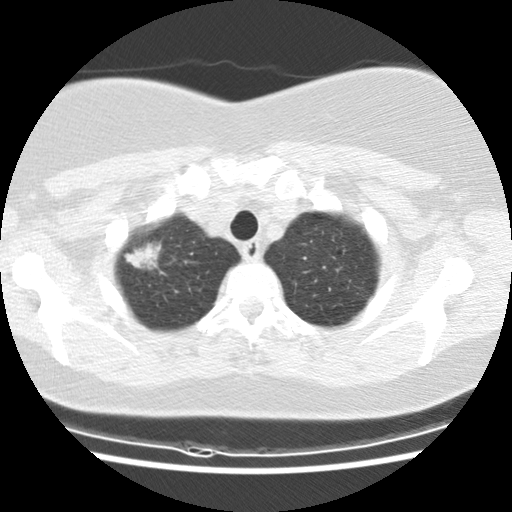
Low-dose screening chest CT, one axial slice; slice 118 of 132 in the series (ordered by position); reconstruction kernel STANDARD; lung window (W 1500 / L -600 HU); 2.5 mm slice thickness; 512 × 512 image matrix, field of view 326 × 326 mm.
Annotated regions visible in this slice (outlined manually by an expert reader):
- lesion 1 (tumor, upper lobe of right lung): box from (x=124, y=242) to (x=161, y=270) px